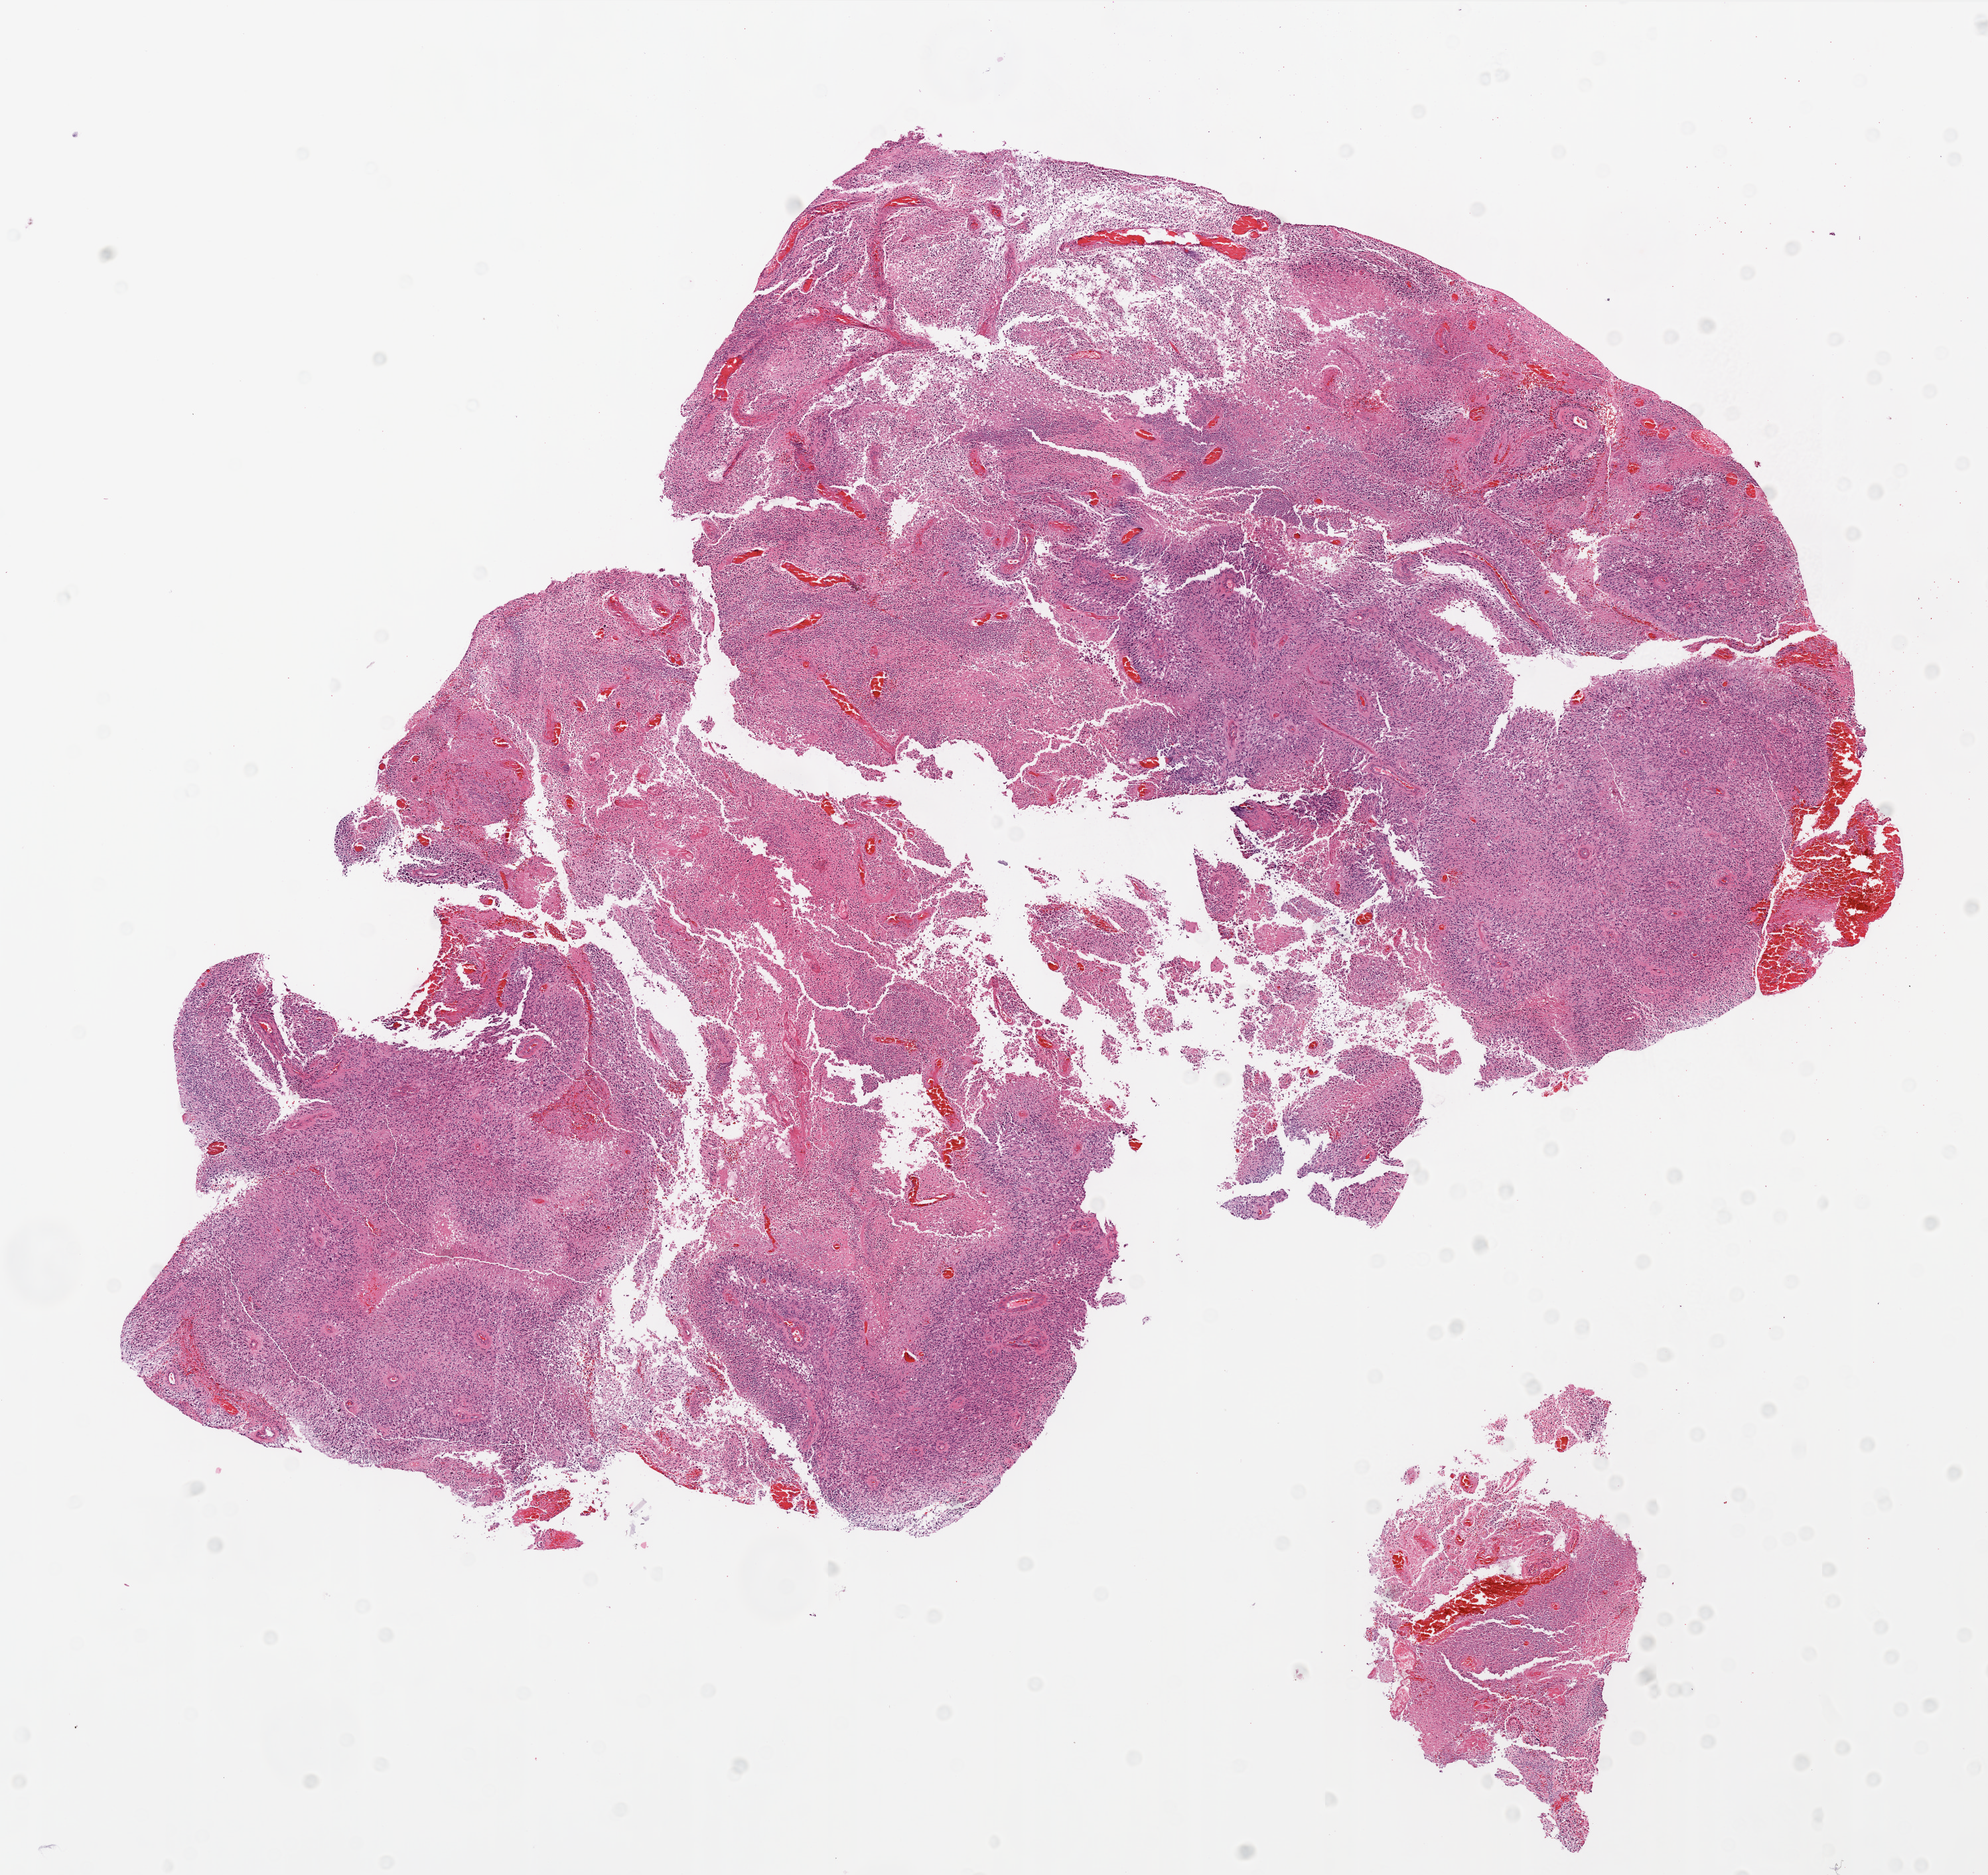
Whole-slide histology image, Hematoxylin and eosin (H&E) stained, low-resolution overview of the scanned area, about 12.0 x 11.3 mm (from a 20x scan); FFPE section; sample: primary tumour, brain. Female patient; age at initial diagnosis 72 years.
Pathologic diagnosis: Glioblastoma.